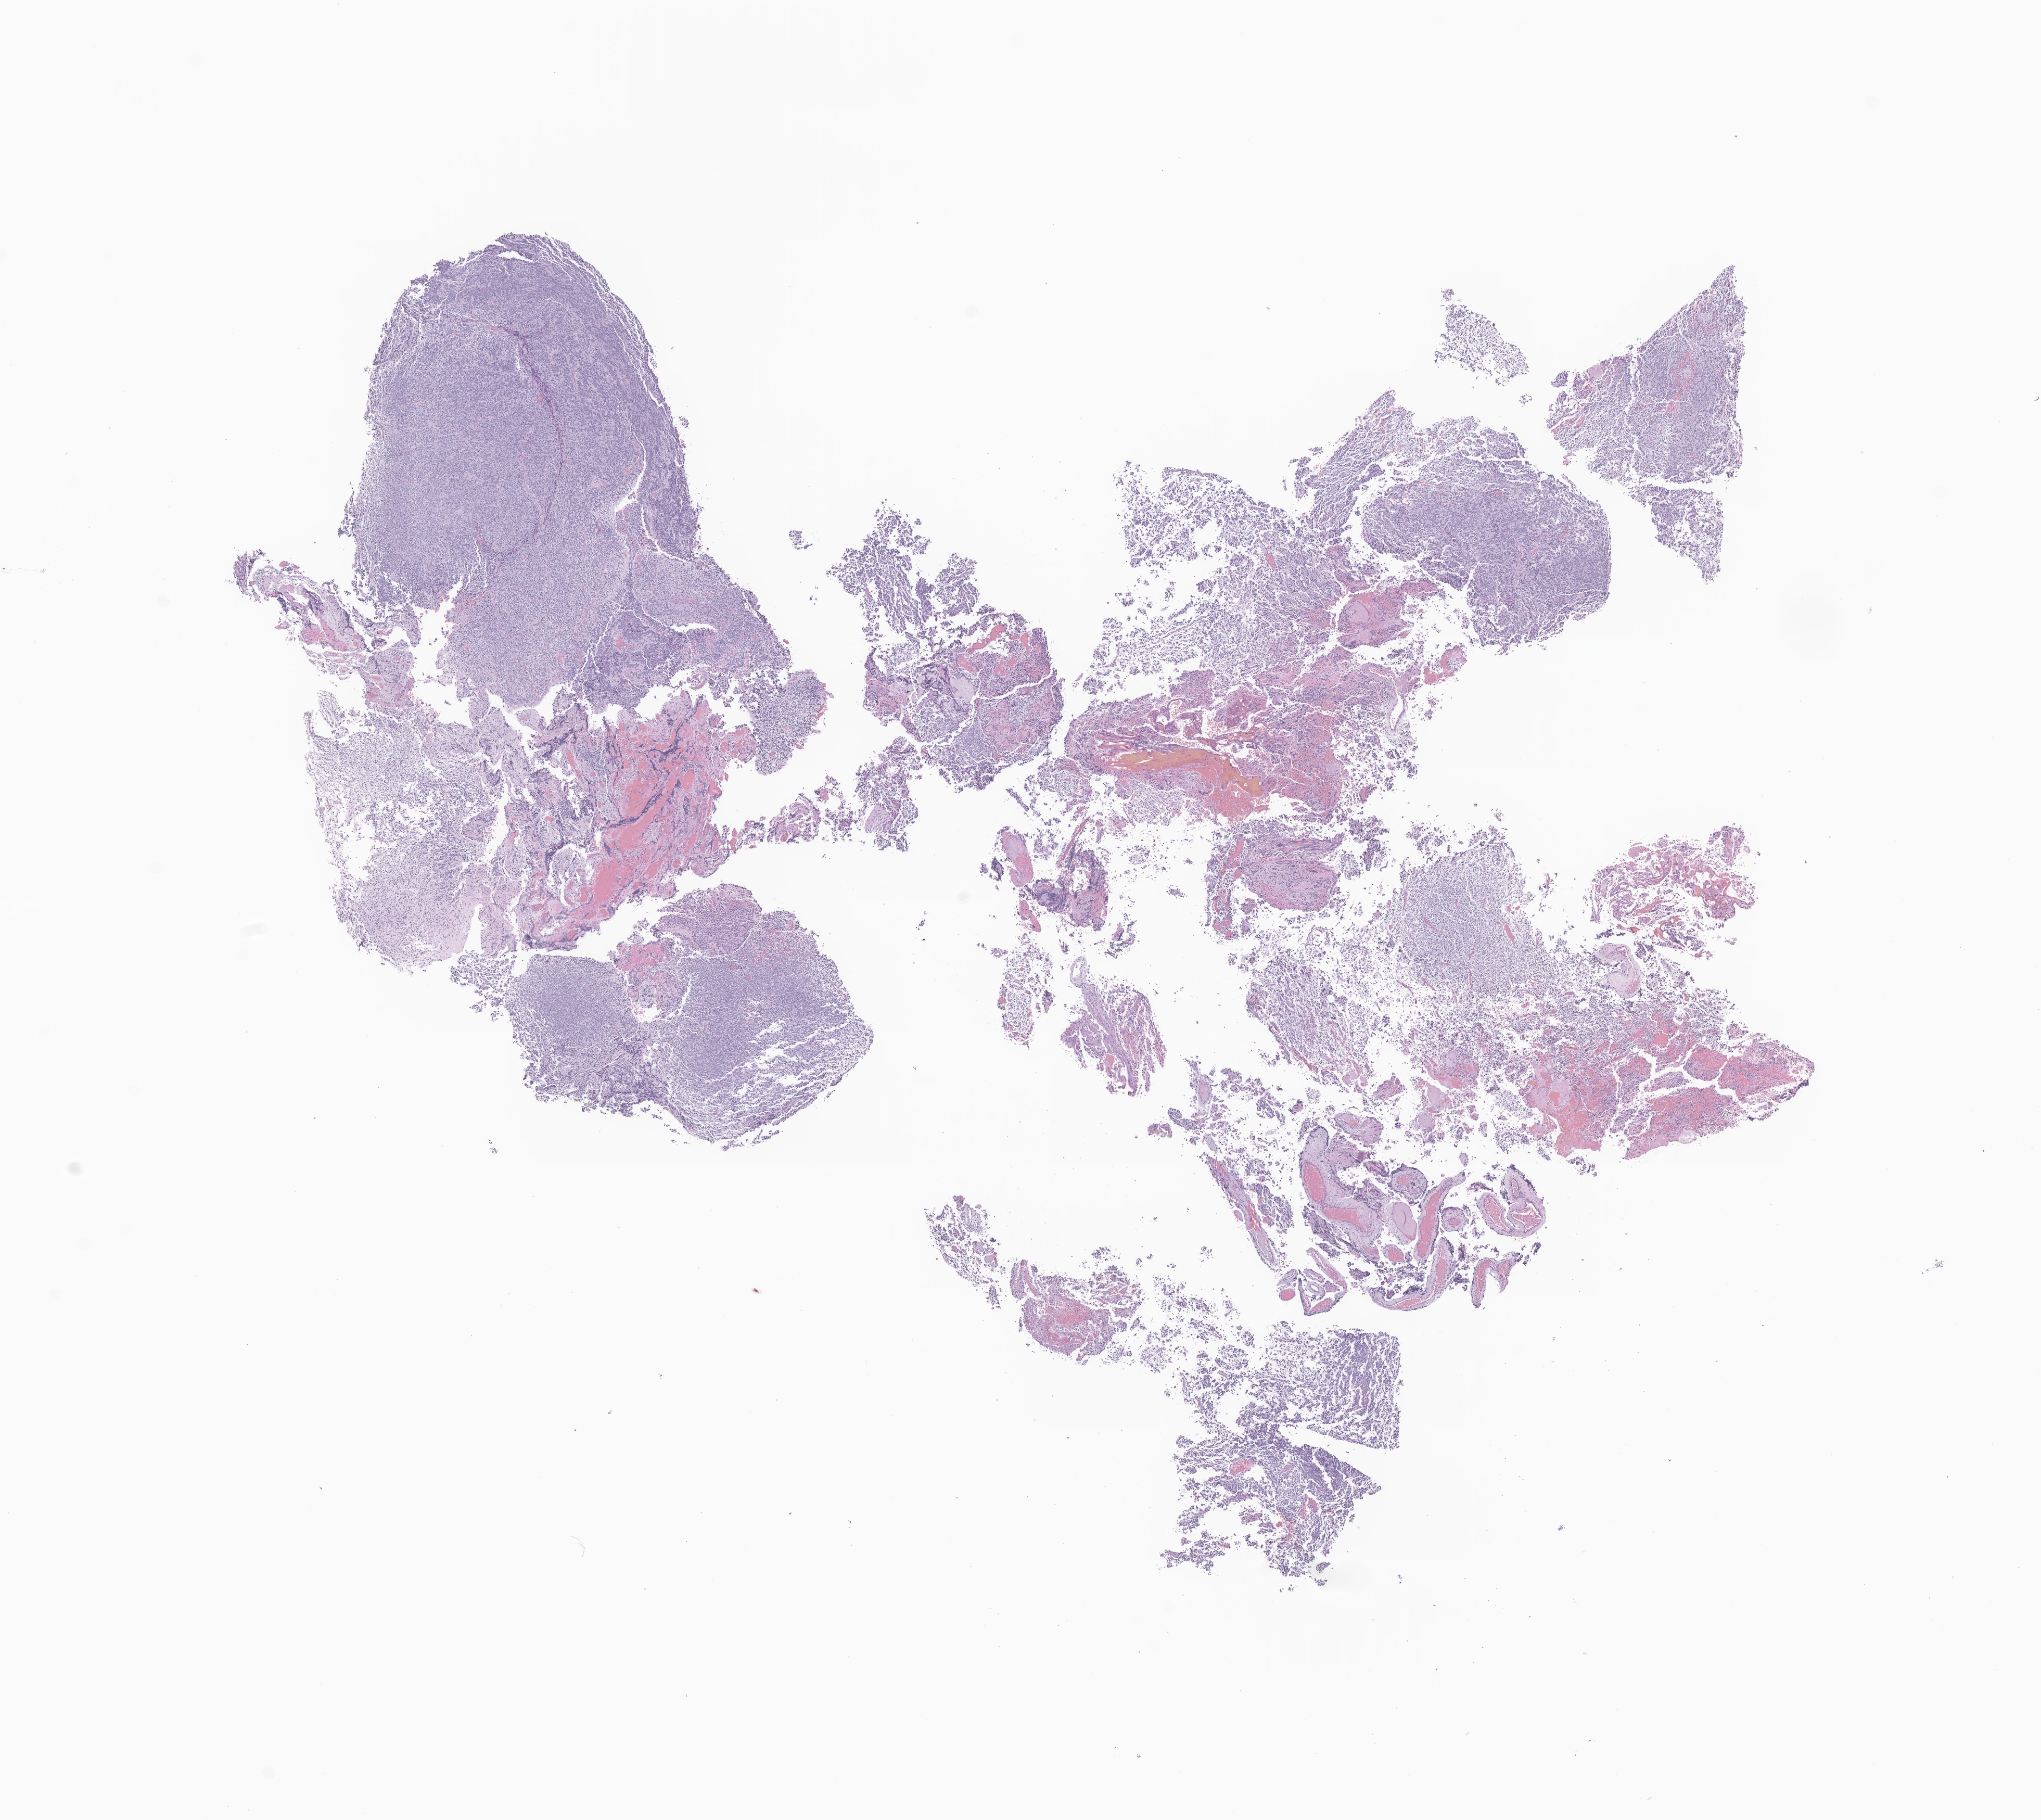
Digitized haematoxylin and eosin-stained section of tumor tissue from the brain, a low-resolution overview of the entire scanned area, about 16.5 x 14.7 mm, formalin-fixed, paraffin-embedded (FFPE) tissue. Patient male; age 59 months (4 years 11 months).
Recorded diagnosis: Neuroblastoma, NOS.